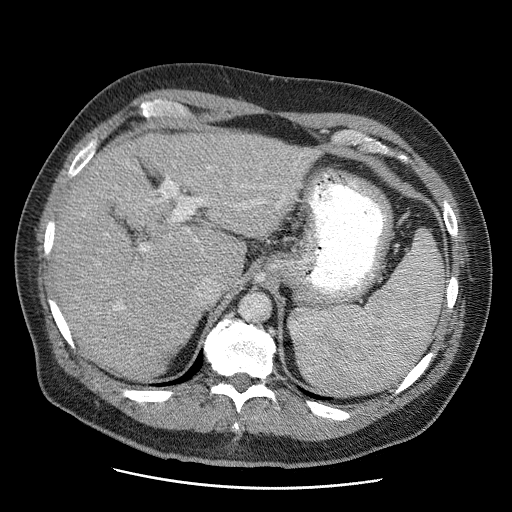
Contrast-enhanced abdominal CT (liver protocol), one axial slice; slice 38 of 81 in the series (ordered by position); soft-tissue window (W 400 / L 40 HU); 2.5 mm slice thickness; 512 × 512 image matrix, field of view 380 × 380 mm. From the clinical record (not read from this slice): diagnosis: hepatocellular carcinoma (patient treated with transarterial chemoembolisation; whether this scan precedes or follows treatment is not stated here); TNM stage (as recorded): Stage-IIIA; Child-Pugh class: A; tumour differentiation: moderately differentiated; tumour nodularity: multinodular.
Annotated regions visible in this slice (semi-automatic segmentation, software-assisted and operator-edited):
- liver parenchyma outside the tumour (the mass and vessels are separate outlines, so this box may not span the whole liver): bounding box [x1, y1, x2, y2] px = [50, 130, 317, 380]
- liver vessels: [114, 167, 285, 310]